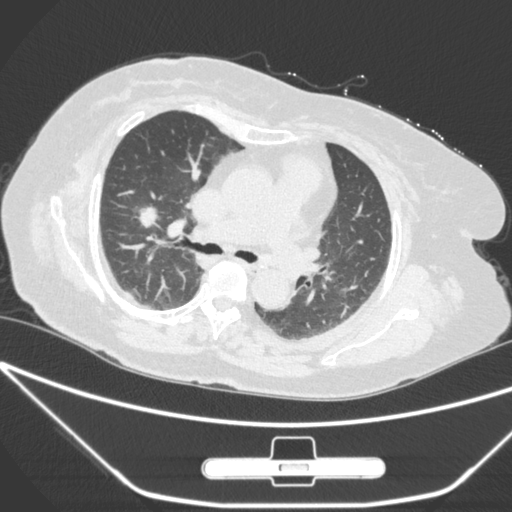
Chest CT, one axial slice. Position 164 of 245 along the scan axis. 120 kVp. Lung window (W 1500 / L -600 HU). 1 mm slice thickness. 512 × 512 image matrix, field of view 365 × 365 mm. Female patient, age 65 years. From the clinical record (not read from this slice): clinical TNM (as recorded): T1c N0 M0; histopathological grade: G3.
Outlined on this slice (rectangle marked by the reading radiologist):
- lung tumour (recorded histology: adenocarcinoma): bounding box [x1, y1, x2, y2] px = [133, 201, 160, 243]